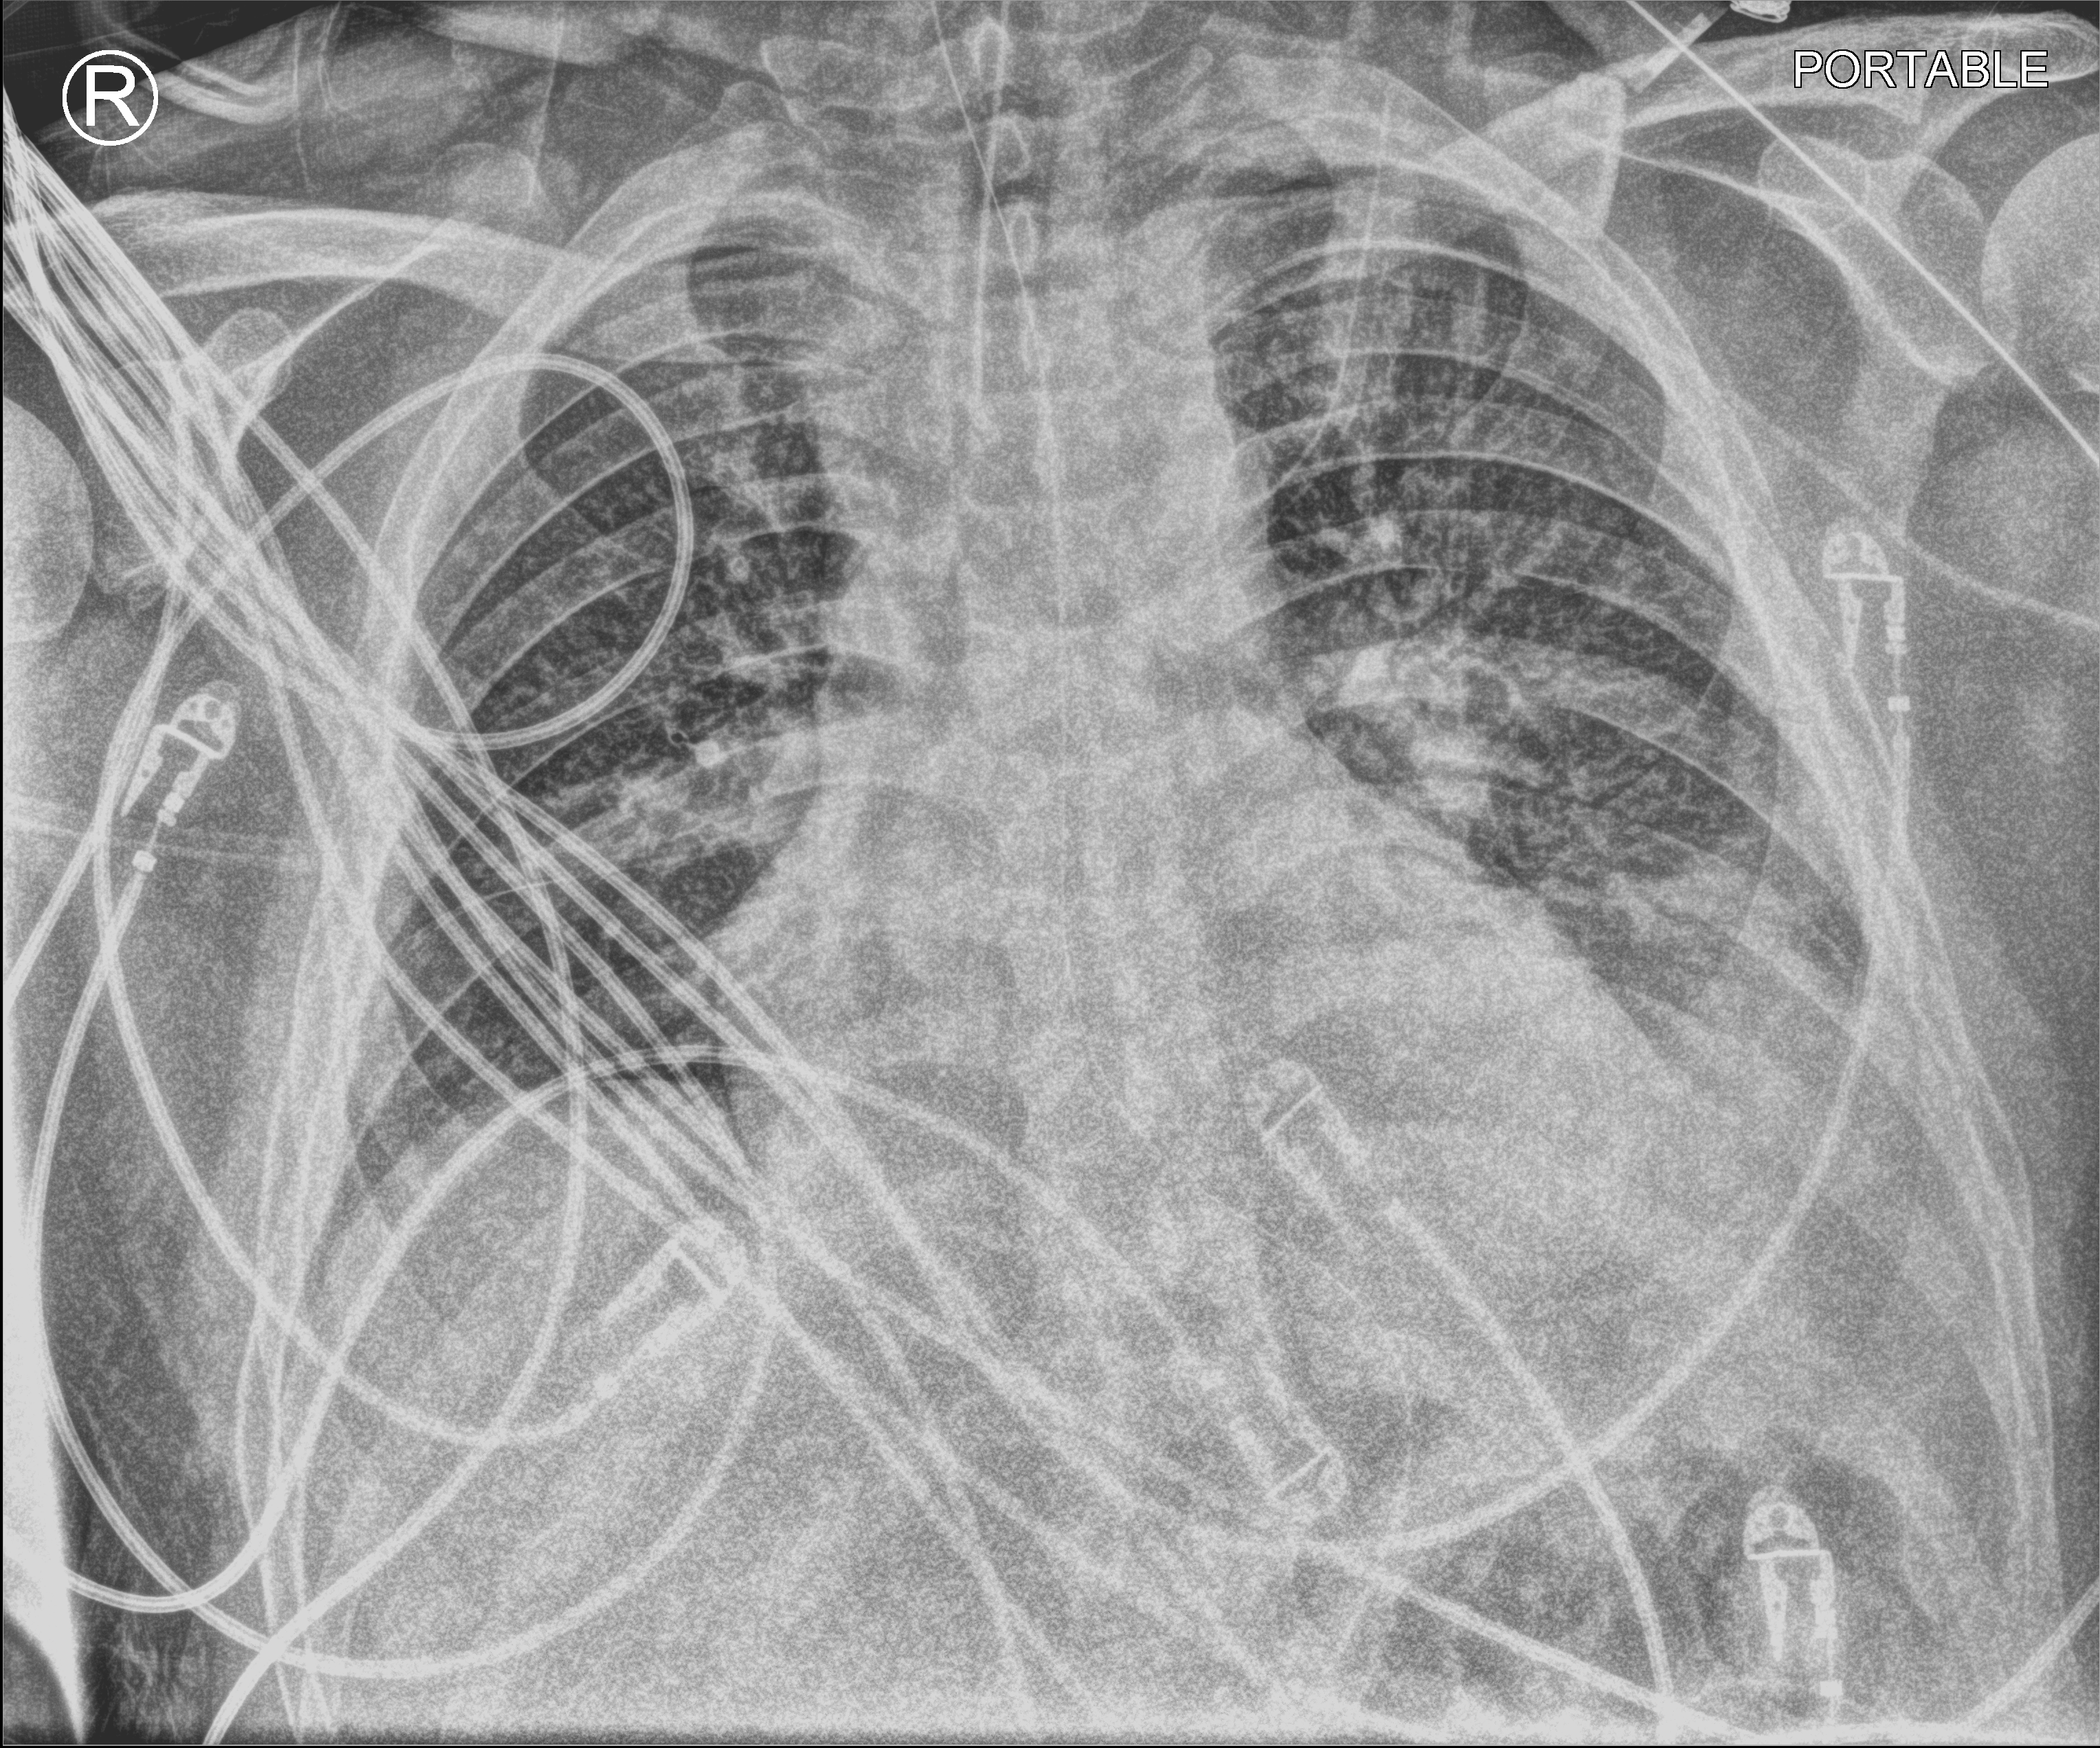
Bedside chest radiograph (computed radiography); anteroposterior (AP) projection. Male patient hospitalised with COVID-19, age 18–59 years.
Admission-level facts for this patient (not findings on this image; timing relative to this image not recorded): admitted to intensive care during this hospital stay: yes.